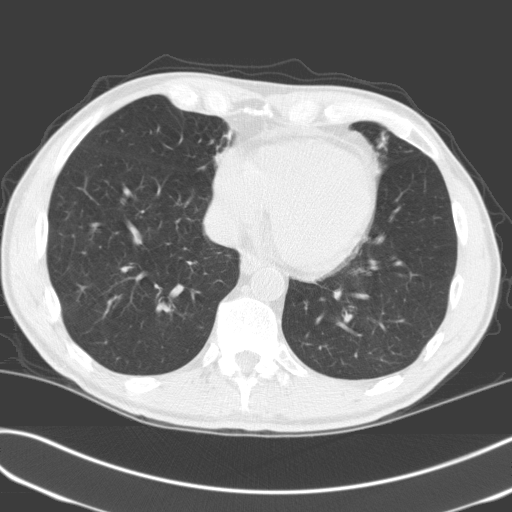
Low-dose screening chest CT, one axial slice; position 57 of 170 along the scan axis; 120 kVp; lung window (W 1500 / L -600 HU); 3.2 mm slice thickness; 512 × 512 image matrix, field of view 351 × 351 mm.
Annotated regions visible in this slice (outlined manually by an expert reader):
- lesion 1 (tumor, upper lobe of left lung): bounding box <379,136,385,148> (left, top, right, bottom; pixels)